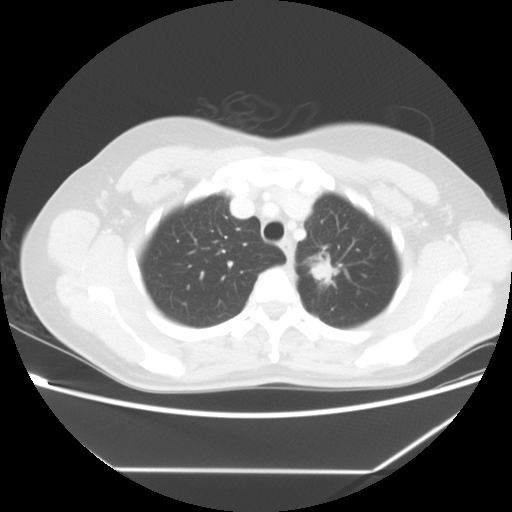
Chest CT, one axial slice; position 48 of 60 along the scan axis; reconstruction kernel STANDARD; lung window (W 1500 / L -600 HU); 512 × 512 image matrix, field of view 367 × 367 mm. Female patient, age 43 years. Case-level facts recorded for this patient, not image findings: clinical TNM (as recorded): T1c N0 M1b.
Annotated regions visible in this slice (bounding box drawn by a radiologist):
- lung tumour (recorded histology: adenocarcinoma): bounding box [x1, y1, x2, y2] px = [301, 257, 339, 293]